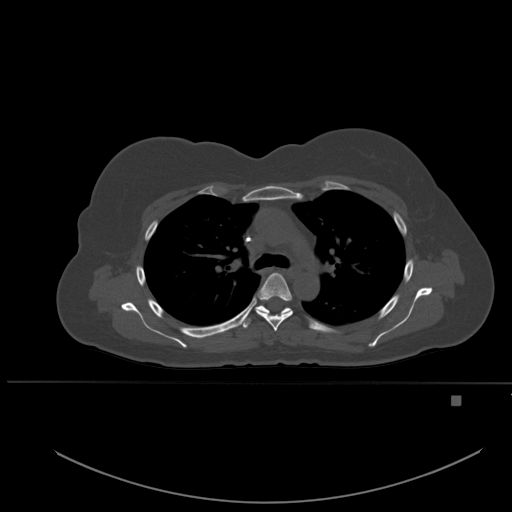
CT including the spine, one axial slice; position 375 of 651 along the scan axis; bone window (W 1800 / L 400 HU); 1.5 mm slice thickness; 512 × 512 image matrix. Patient: female, 49 years. Case-level facts recorded for this patient, not image findings: primary cancer: breast.
Outlined on this slice (semi-automatically segmented with operator editing):
- T4 vertebra: bounding box (x1, y1, x2, y2) in pixels: (255, 273, 293, 331)
- T5 vertebra: (241, 305, 292, 328)